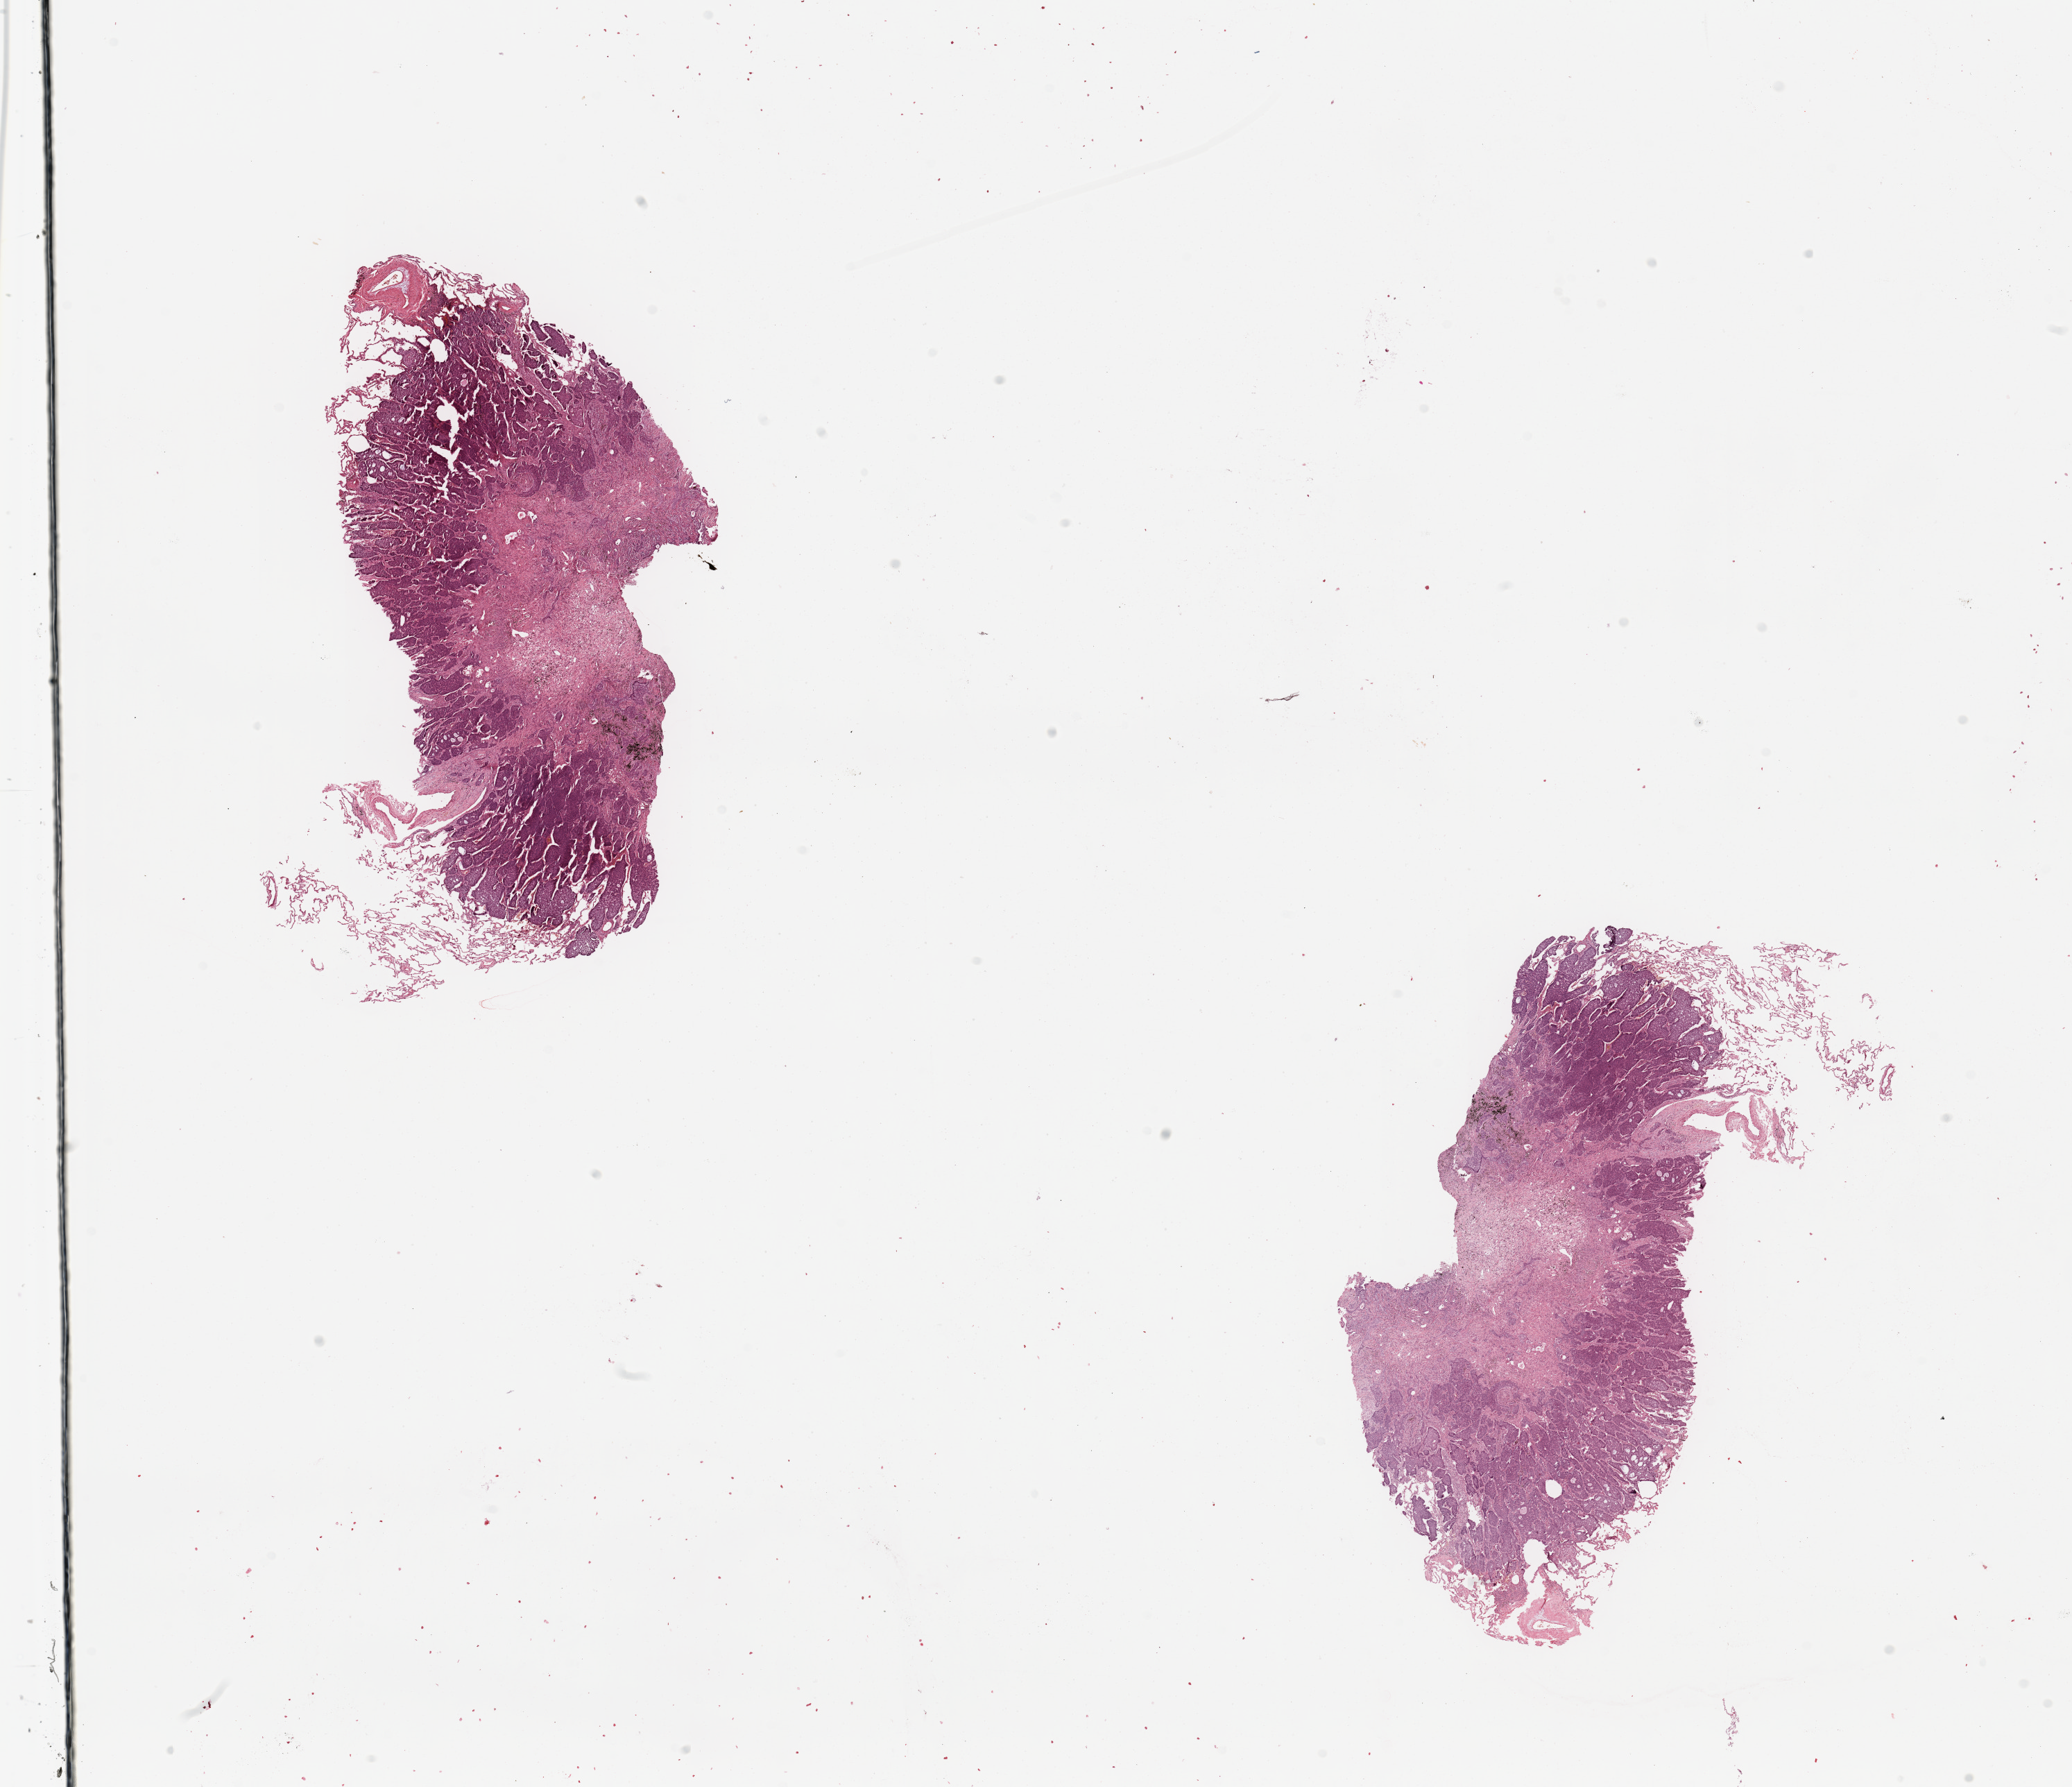
H&E whole-slide image, low-resolution overview of the scanned area, about 23.6 x 20.4 mm, tumour tissue sample, lung. 66-year-old male patient.
Patient diagnosis (cohort enrolment): squamous cell carcinoma (lung).